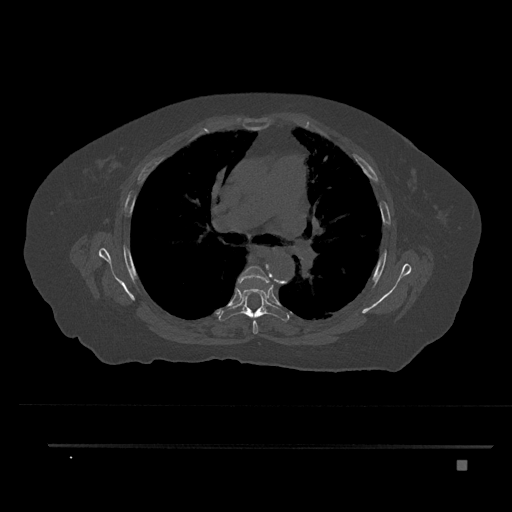
CT including the spine, one axial slice. Position 540 of 797 along the scan axis. Reconstruction kernel Br40s/3. Bone window (W 1800 / L 400 HU). 0.5 mm slice thickness. 512 × 512 image matrix. Female patient, age 76 years. From the clinical record (not read from this slice): primary cancer: lung.
Outlined on this slice (semi-automatically segmented with operator editing):
- T5 vertebra: box from (x=237, y=266) to (x=270, y=334) px
- T6 vertebra: (x=219, y=281)–(x=290, y=322)